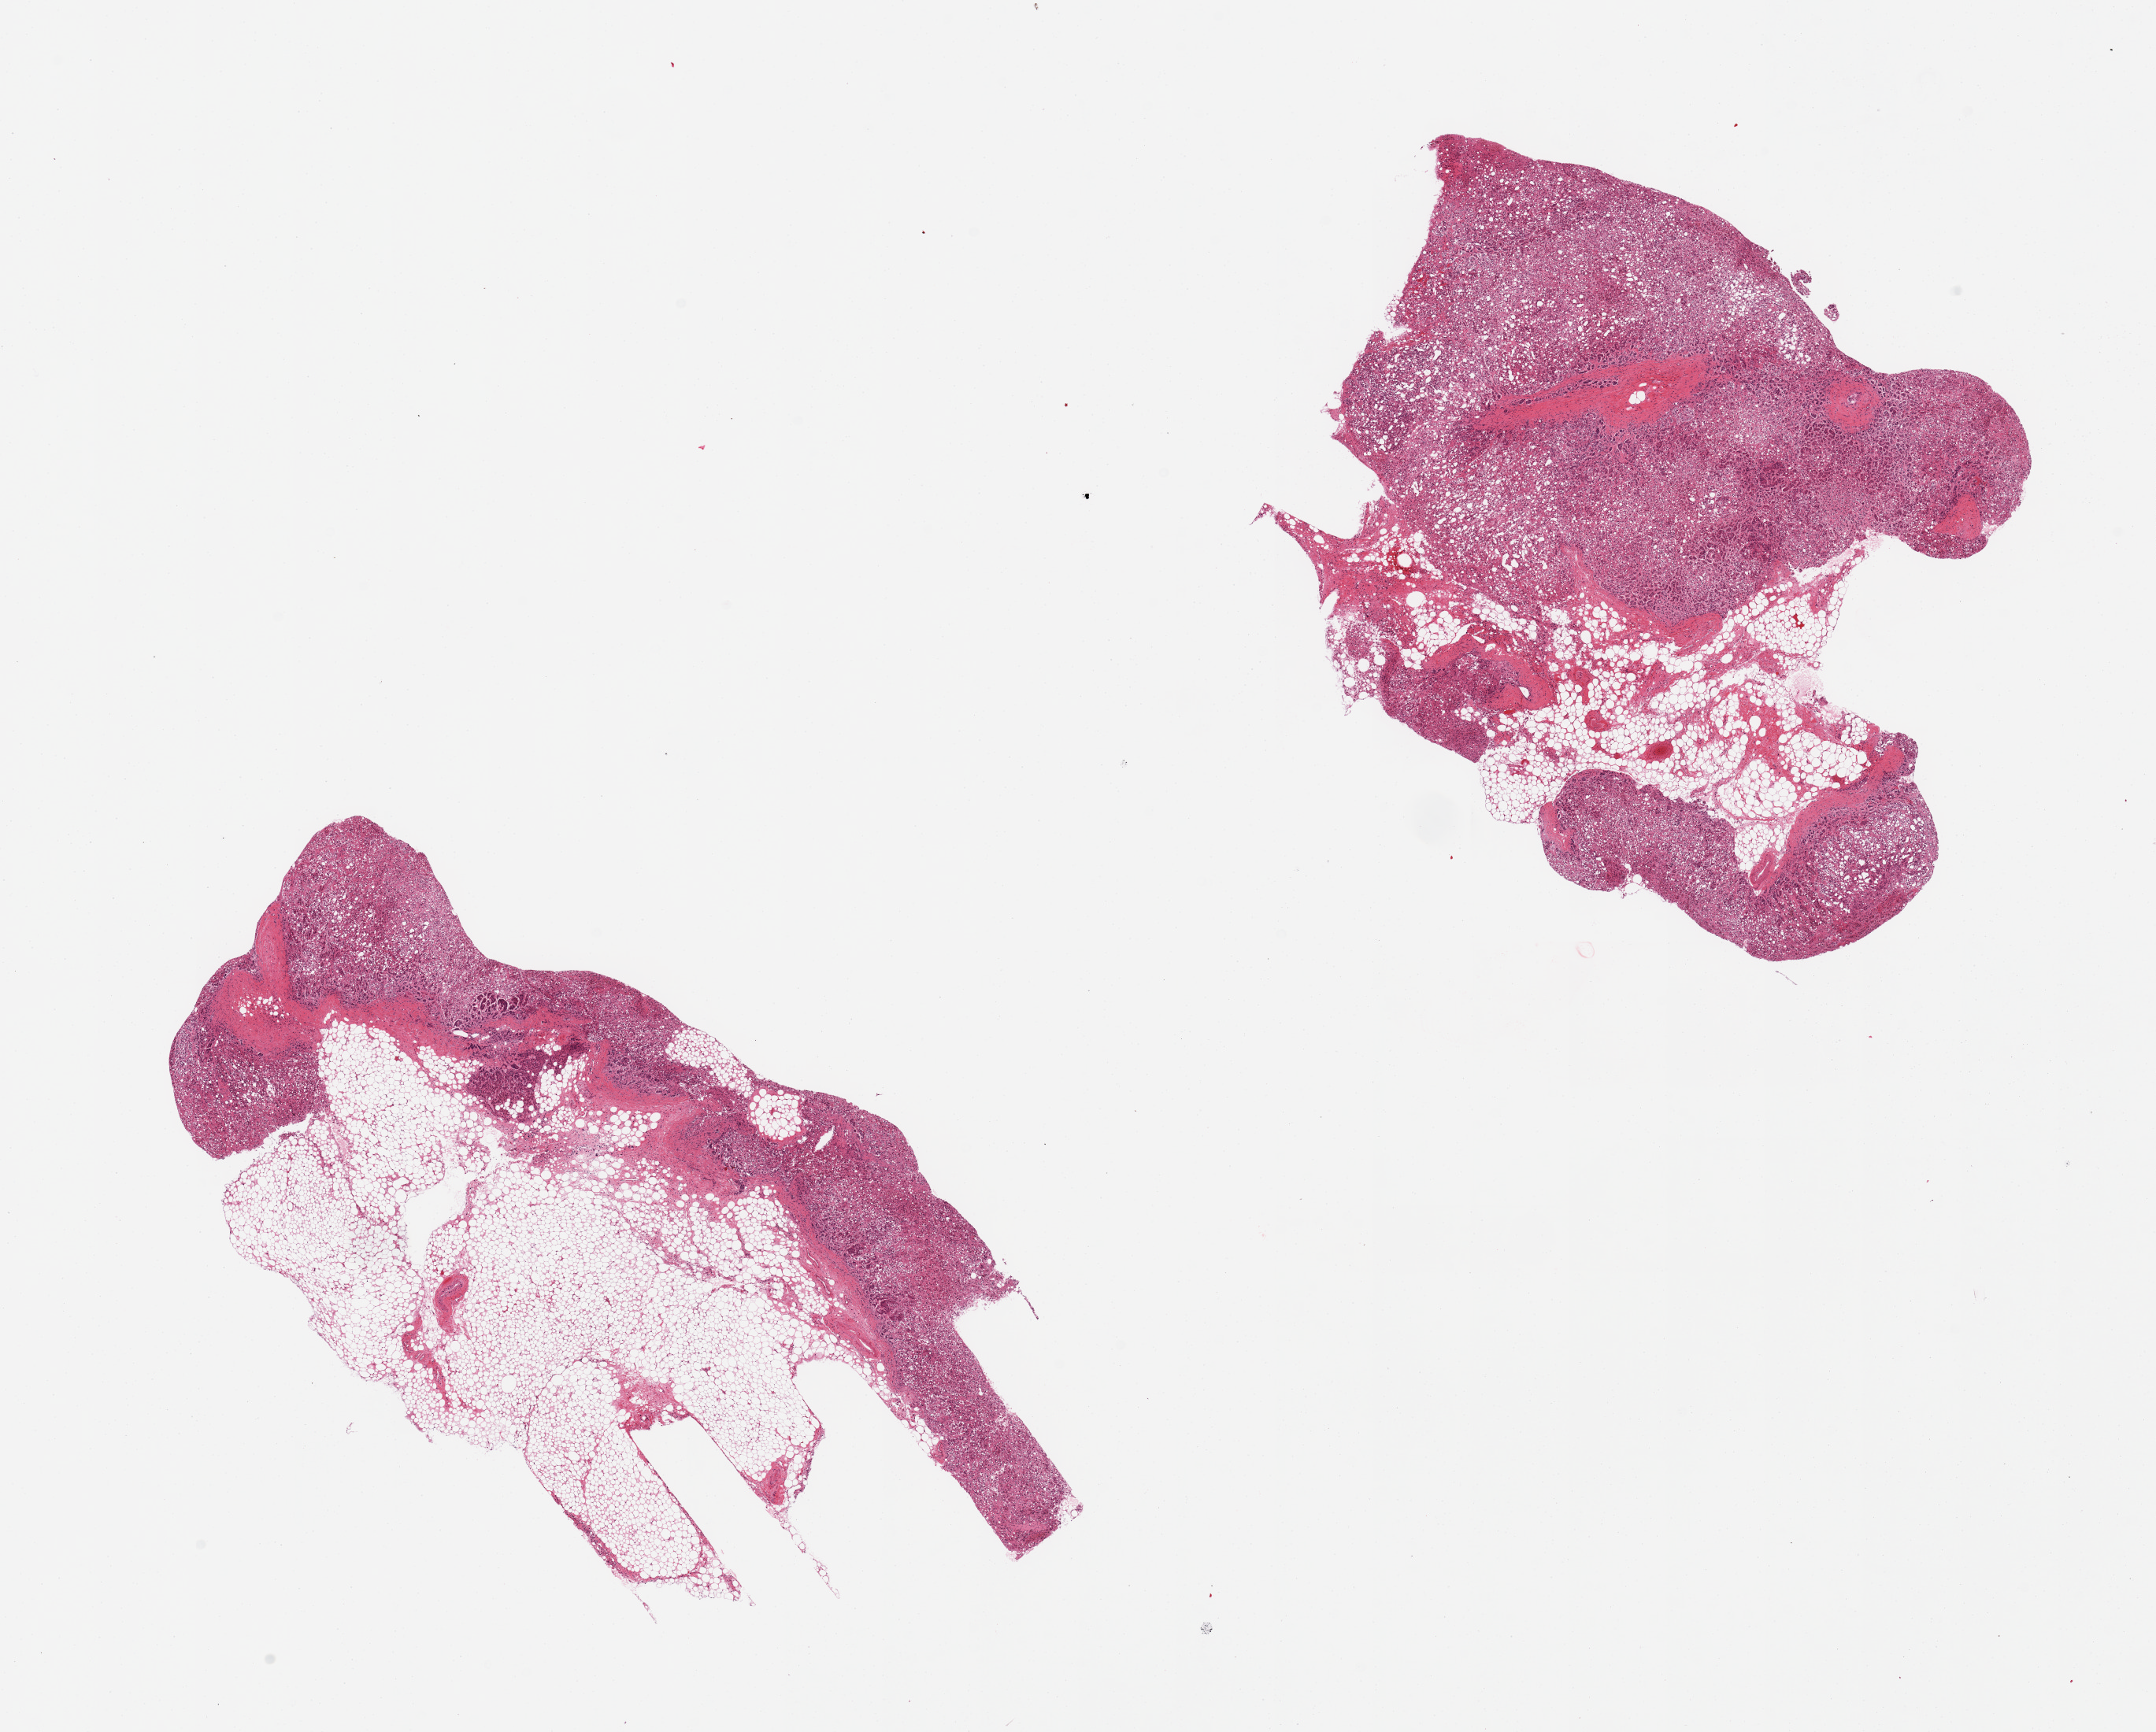
Whole-slide image, hematoxylin and eosin (H&E) stain, brightfield, shown as a low-resolution overview of the whole scanned area (about 21.7 x 17.4 mm, acquisition: 20x scan). PAXgene-fixed paraffin-embedded (PFPE) section. Sampled site (target tissue): adrenal gland. Donor tissue sample. Male donor.
Review note (as recorded): 2 pieces, one is 70% fat, second is 30% fat, severely autolyzed.